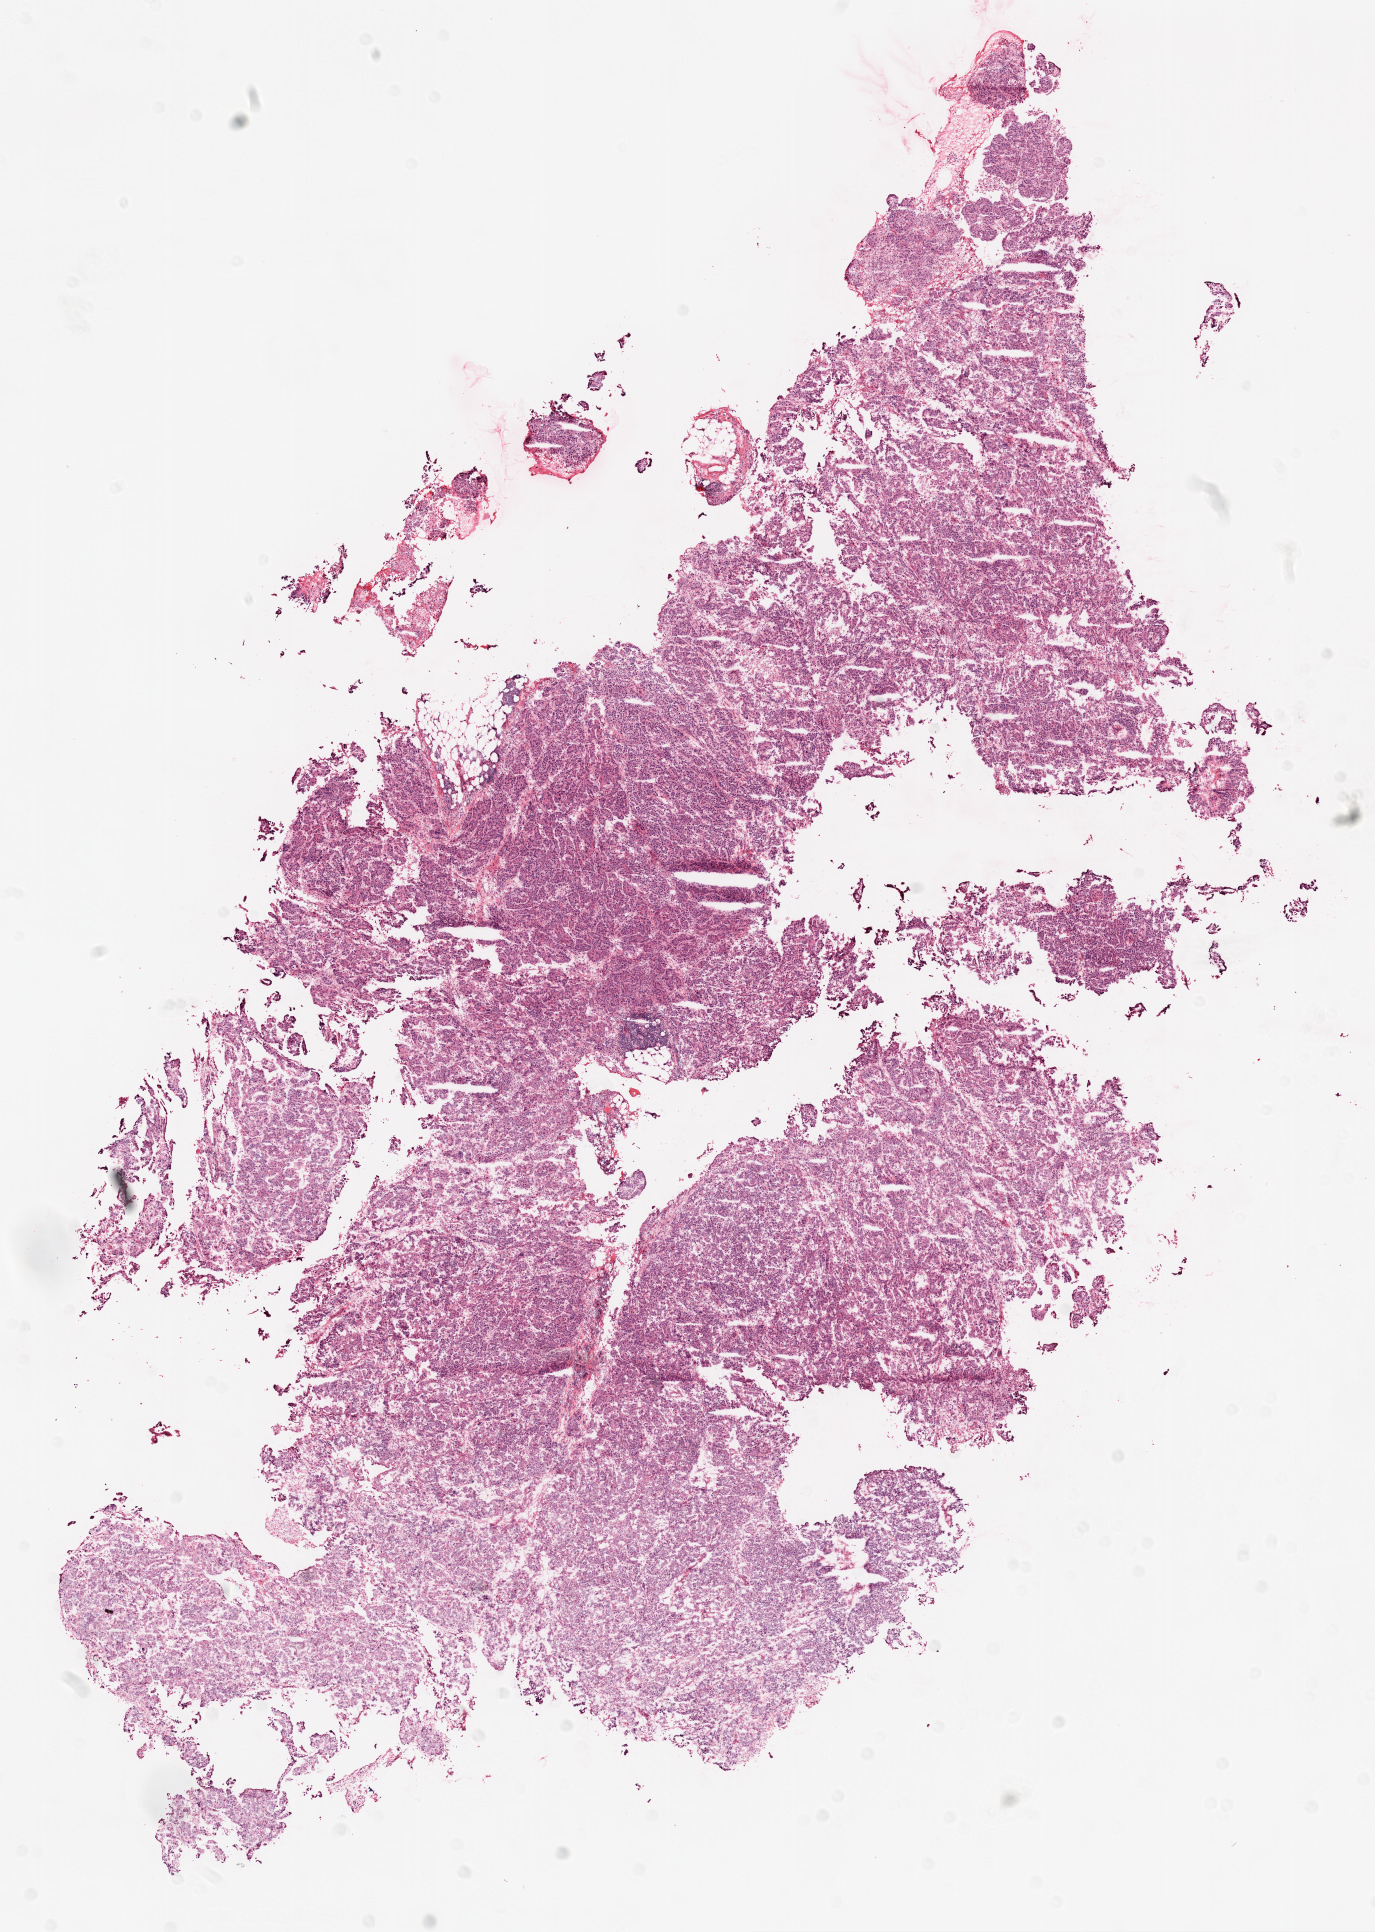
Whole-slide histology image, H&E-stained — shown as a low-resolution overview of the whole scanned area (about 11.0 x 15.5 mm). Frozen section from the top of the tissue portion. Primary tumour sample from the ovary. Female patient; age at initial diagnosis 57 years. Histologic grade: G3 (poorly differentiated). Slide review estimates, as recorded: tumour cells 98%, tumour nuclei 90%, normal cells 0%, stromal cells 0%, necrosis 2%.
Laterality: bilateral. FIGO stage: IIIC. Histologic diagnosis: Serous cystadenocarcinoma, NOS.